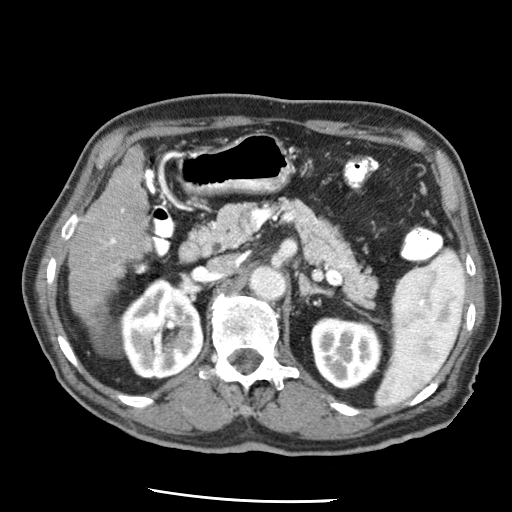
Contrast-enhanced abdominal CT (liver protocol), one axial slice. 120 kVp. Soft-tissue window (W 400 / L 40 HU). 2.5 mm slice thickness. 512 × 512 image matrix, field of view 320 × 320 mm. Case-level facts recorded for this patient, not image findings: diagnosis: hepatocellular carcinoma (patient treated with transarterial chemoembolisation; whether this scan precedes or follows treatment is not stated here); TNM stage (as recorded): Stage-IIIA; Child-Pugh class: A.
Outlined on this slice (semi-automatic segmentation, software-assisted and operator-edited):
- liver parenchyma outside the tumour (the mass and vessels are separate outlines, so this box may not span the whole liver): box from (x=68, y=148) to (x=148, y=326) px
- liver vessels: (x=105, y=209)–(x=125, y=266)